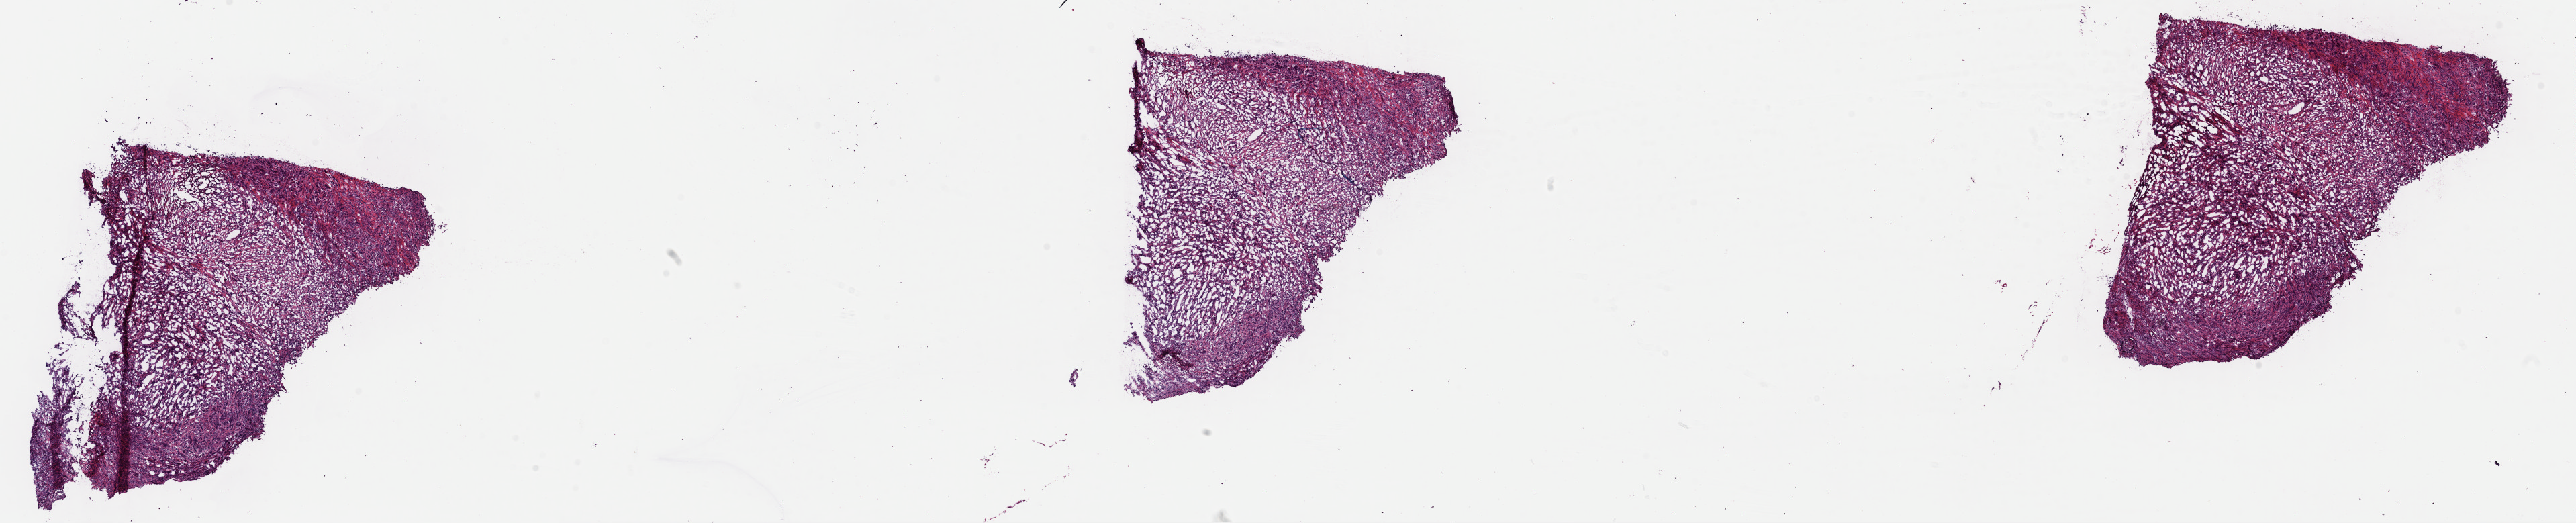
Digitized H&E tissue section (whole slide), shown as a low-resolution overview of the whole scanned area (about 30.3 x 6.2 mm, from a 40x scan). Frozen section from the top of the tissue portion. Metastatic tumour sample, sampled site not recorded. Patient: male, age at initial diagnosis 53 years. Pathologist review of this section (percent, as recorded): tumour cells 85%, tumour nuclei 85%, normal cells 0%, stromal cells 15%, necrosis 0%. Inflammatory infiltration, as recorded: lymphocyte infiltration 1%, monocyte infiltration 1%, neutrophil infiltration 1%.
This section: metastatic tumour tissue. Patient diagnosis: Malignant melanoma, NOS.